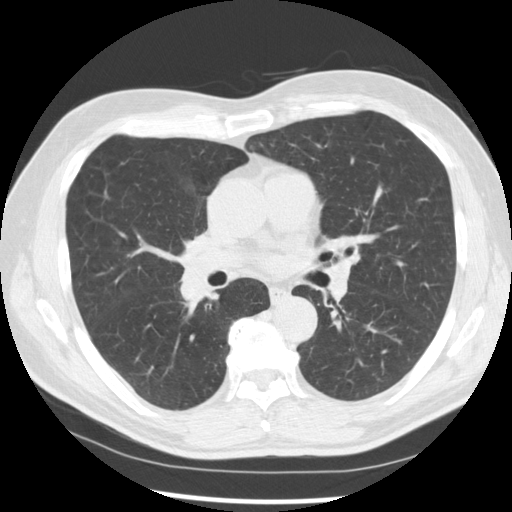
Low-dose screening chest CT, axial slice. First (baseline) screen. Lung window (W 1500 / L -600 HU). 2.5 mm slice thickness. Standard (soft-tissue) reconstruction kernel (STANDARD). Slice 155 of 277 in the series. Male, age 67 years at enrolment. Current smoker at enrolment.
- Expert reader's lesion annotation, bounding box (x1, y1, x2, y2) in pixels: (161, 248, 230, 311).
- Reader record for this screening exam (exam-level; its link to the box is not recorded): non-calcified nodule or mass ≥4 mm, left lower lobe, 15 × 15 mm, spiculated (stellate) margins, soft tissue attenuation.
- Note: the box lies in the patient's right hemithorax on this image, whereas the reader's record names the left lung; they may be different findings.
- Official screen result: positive, change unspecified: nodule(s) >= 4 mm or enlarging nodule(s), mass(es), or other non-specific abnormalities suspicious for lung cancer.